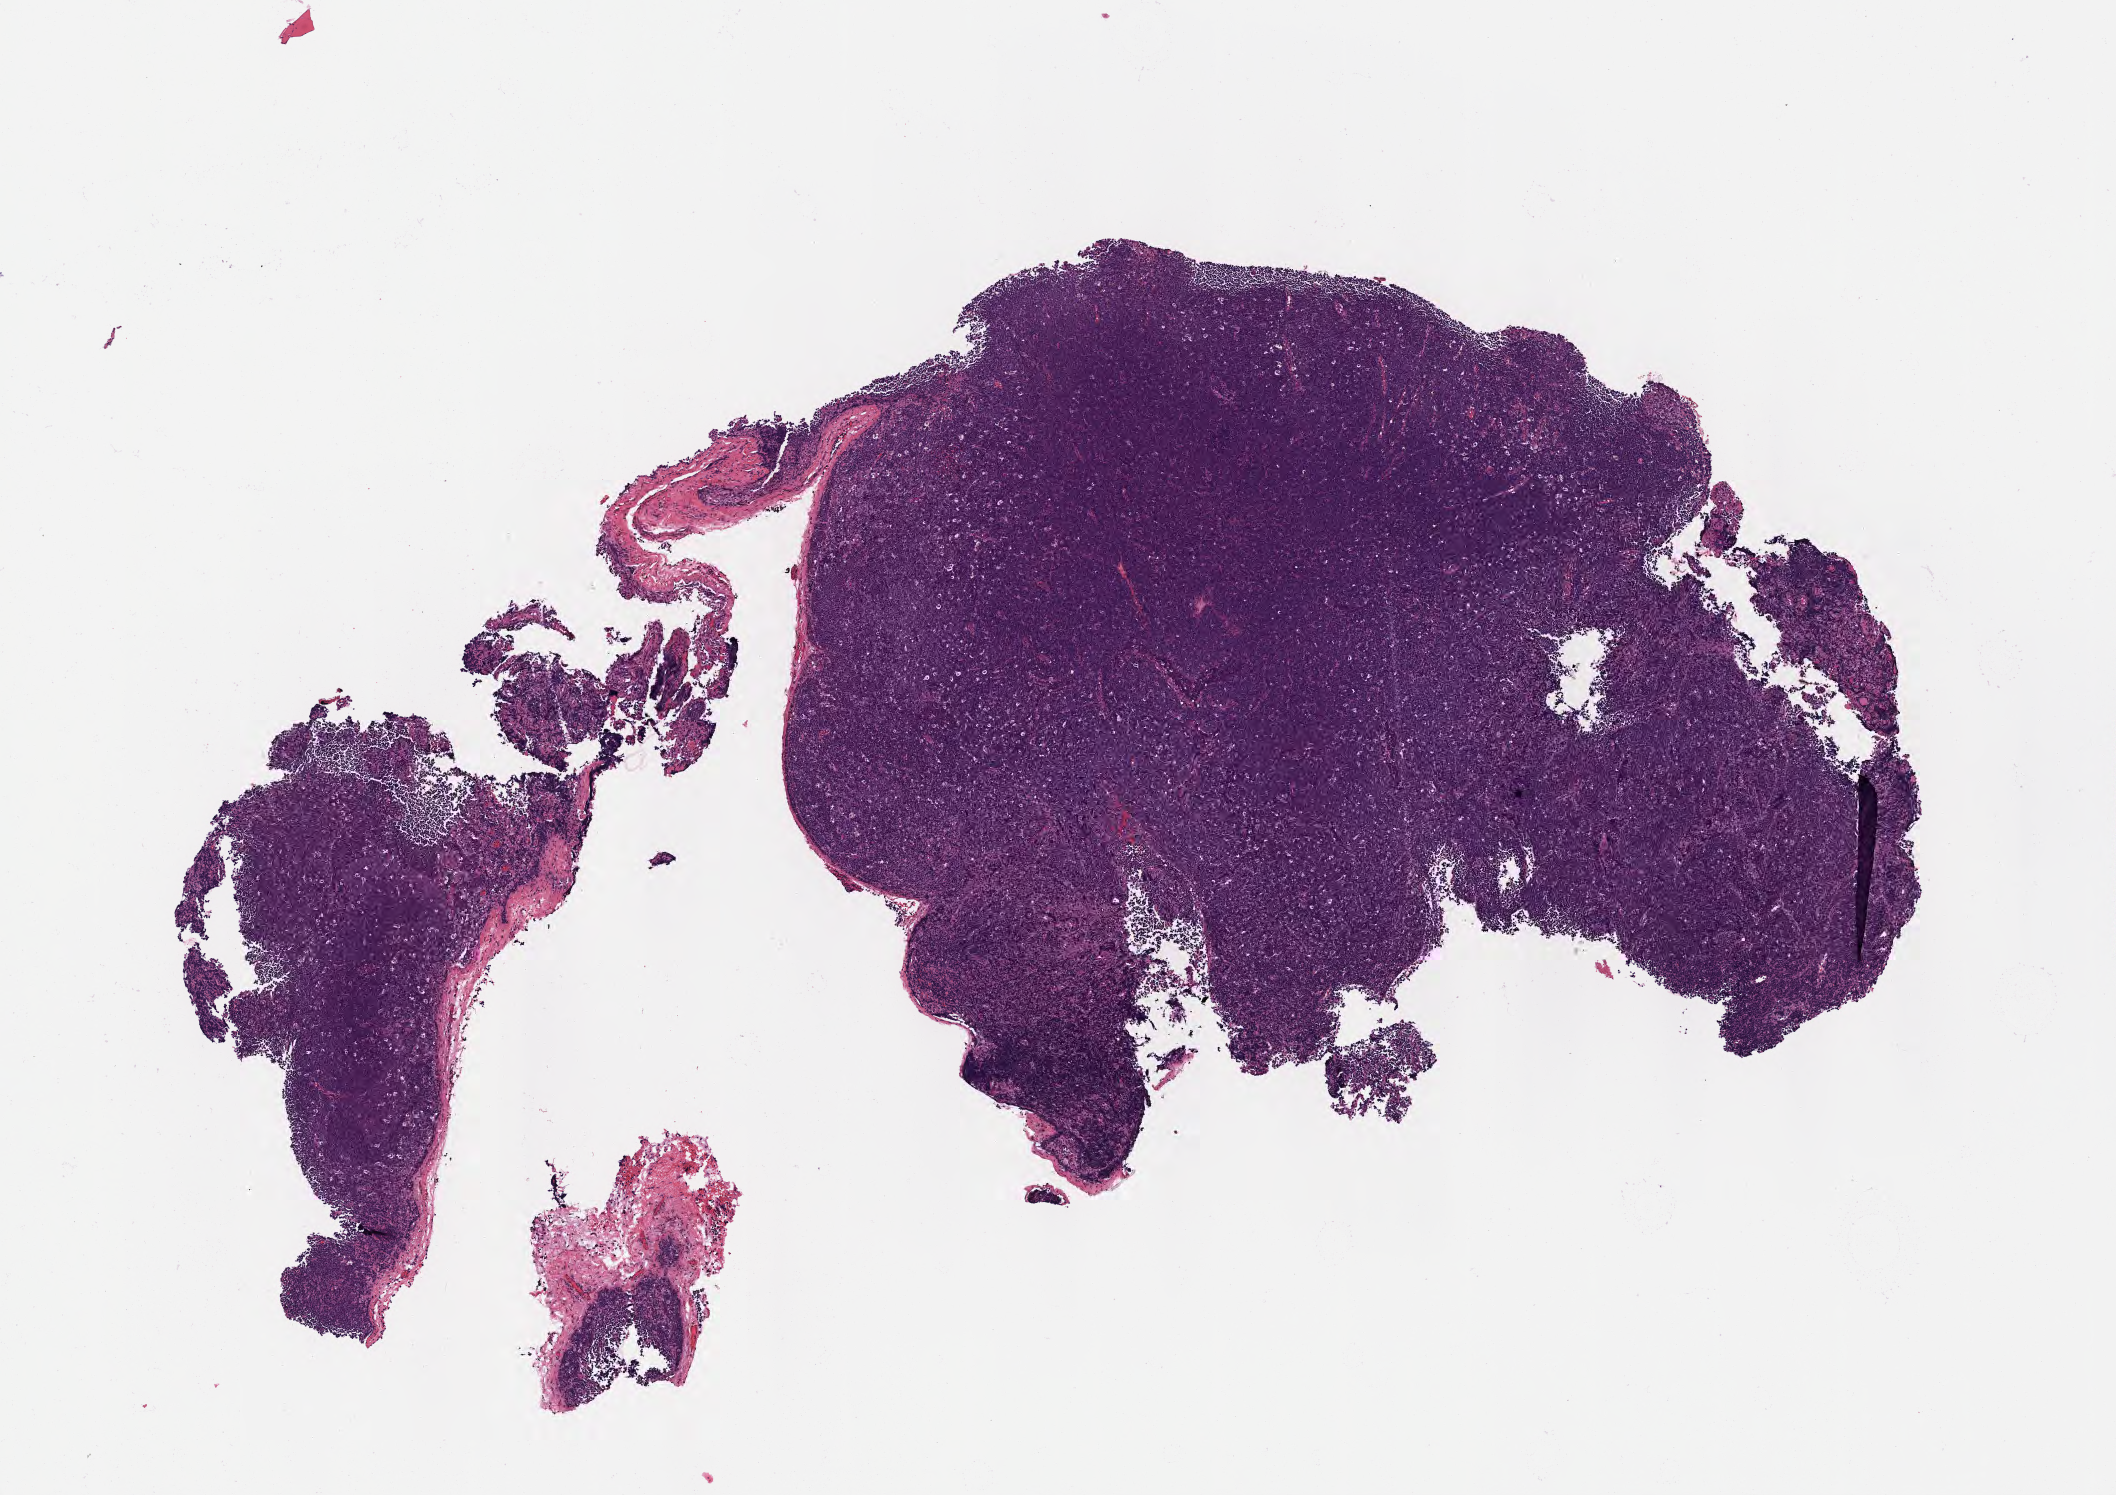
Digitized haematoxylin and eosin-stained section — whole scanned area (about 8.6 x 6.0 mm) shown as a low-resolution overview, formalin-fixed, paraffin-embedded (FFPE) tissue, specimen: primary tumor, anatomic site: lymph node of head and neck. Patient: female, age at initial diagnosis 8 years. Composition of this section per pathologist review: tumor cells 90%, tumor nuclei 95%, stromal cells 5%, necrosis 5%, normal cells 0%. Infiltration values recorded for this section: lymphocyte infiltration 50%, monocyte infiltration 30%, neutrophil infiltration 5%.
Diagnosis: Burkitt lymphoma, NOS. Section: top of the tissue portion.